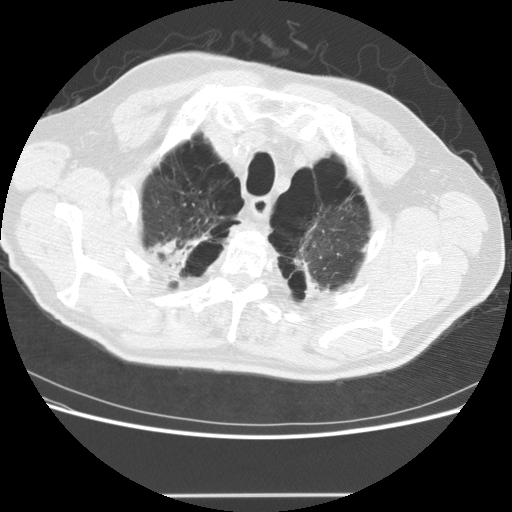
Low-dose screening chest CT, one axial slice. Slice 125 of 151 in the series (ordered by position). Reconstruction kernel STANDARD. 120 kVp. Lung window (W 1500 / L -600 HU). 2.5 mm slice thickness. 512 × 512 image matrix, field of view 360 × 360 mm.
Outlined on this slice (outlined manually by an expert reader):
- lesion 1 (tumor, upper lobe of right lung): box from (x=154, y=237) to (x=190, y=278) px